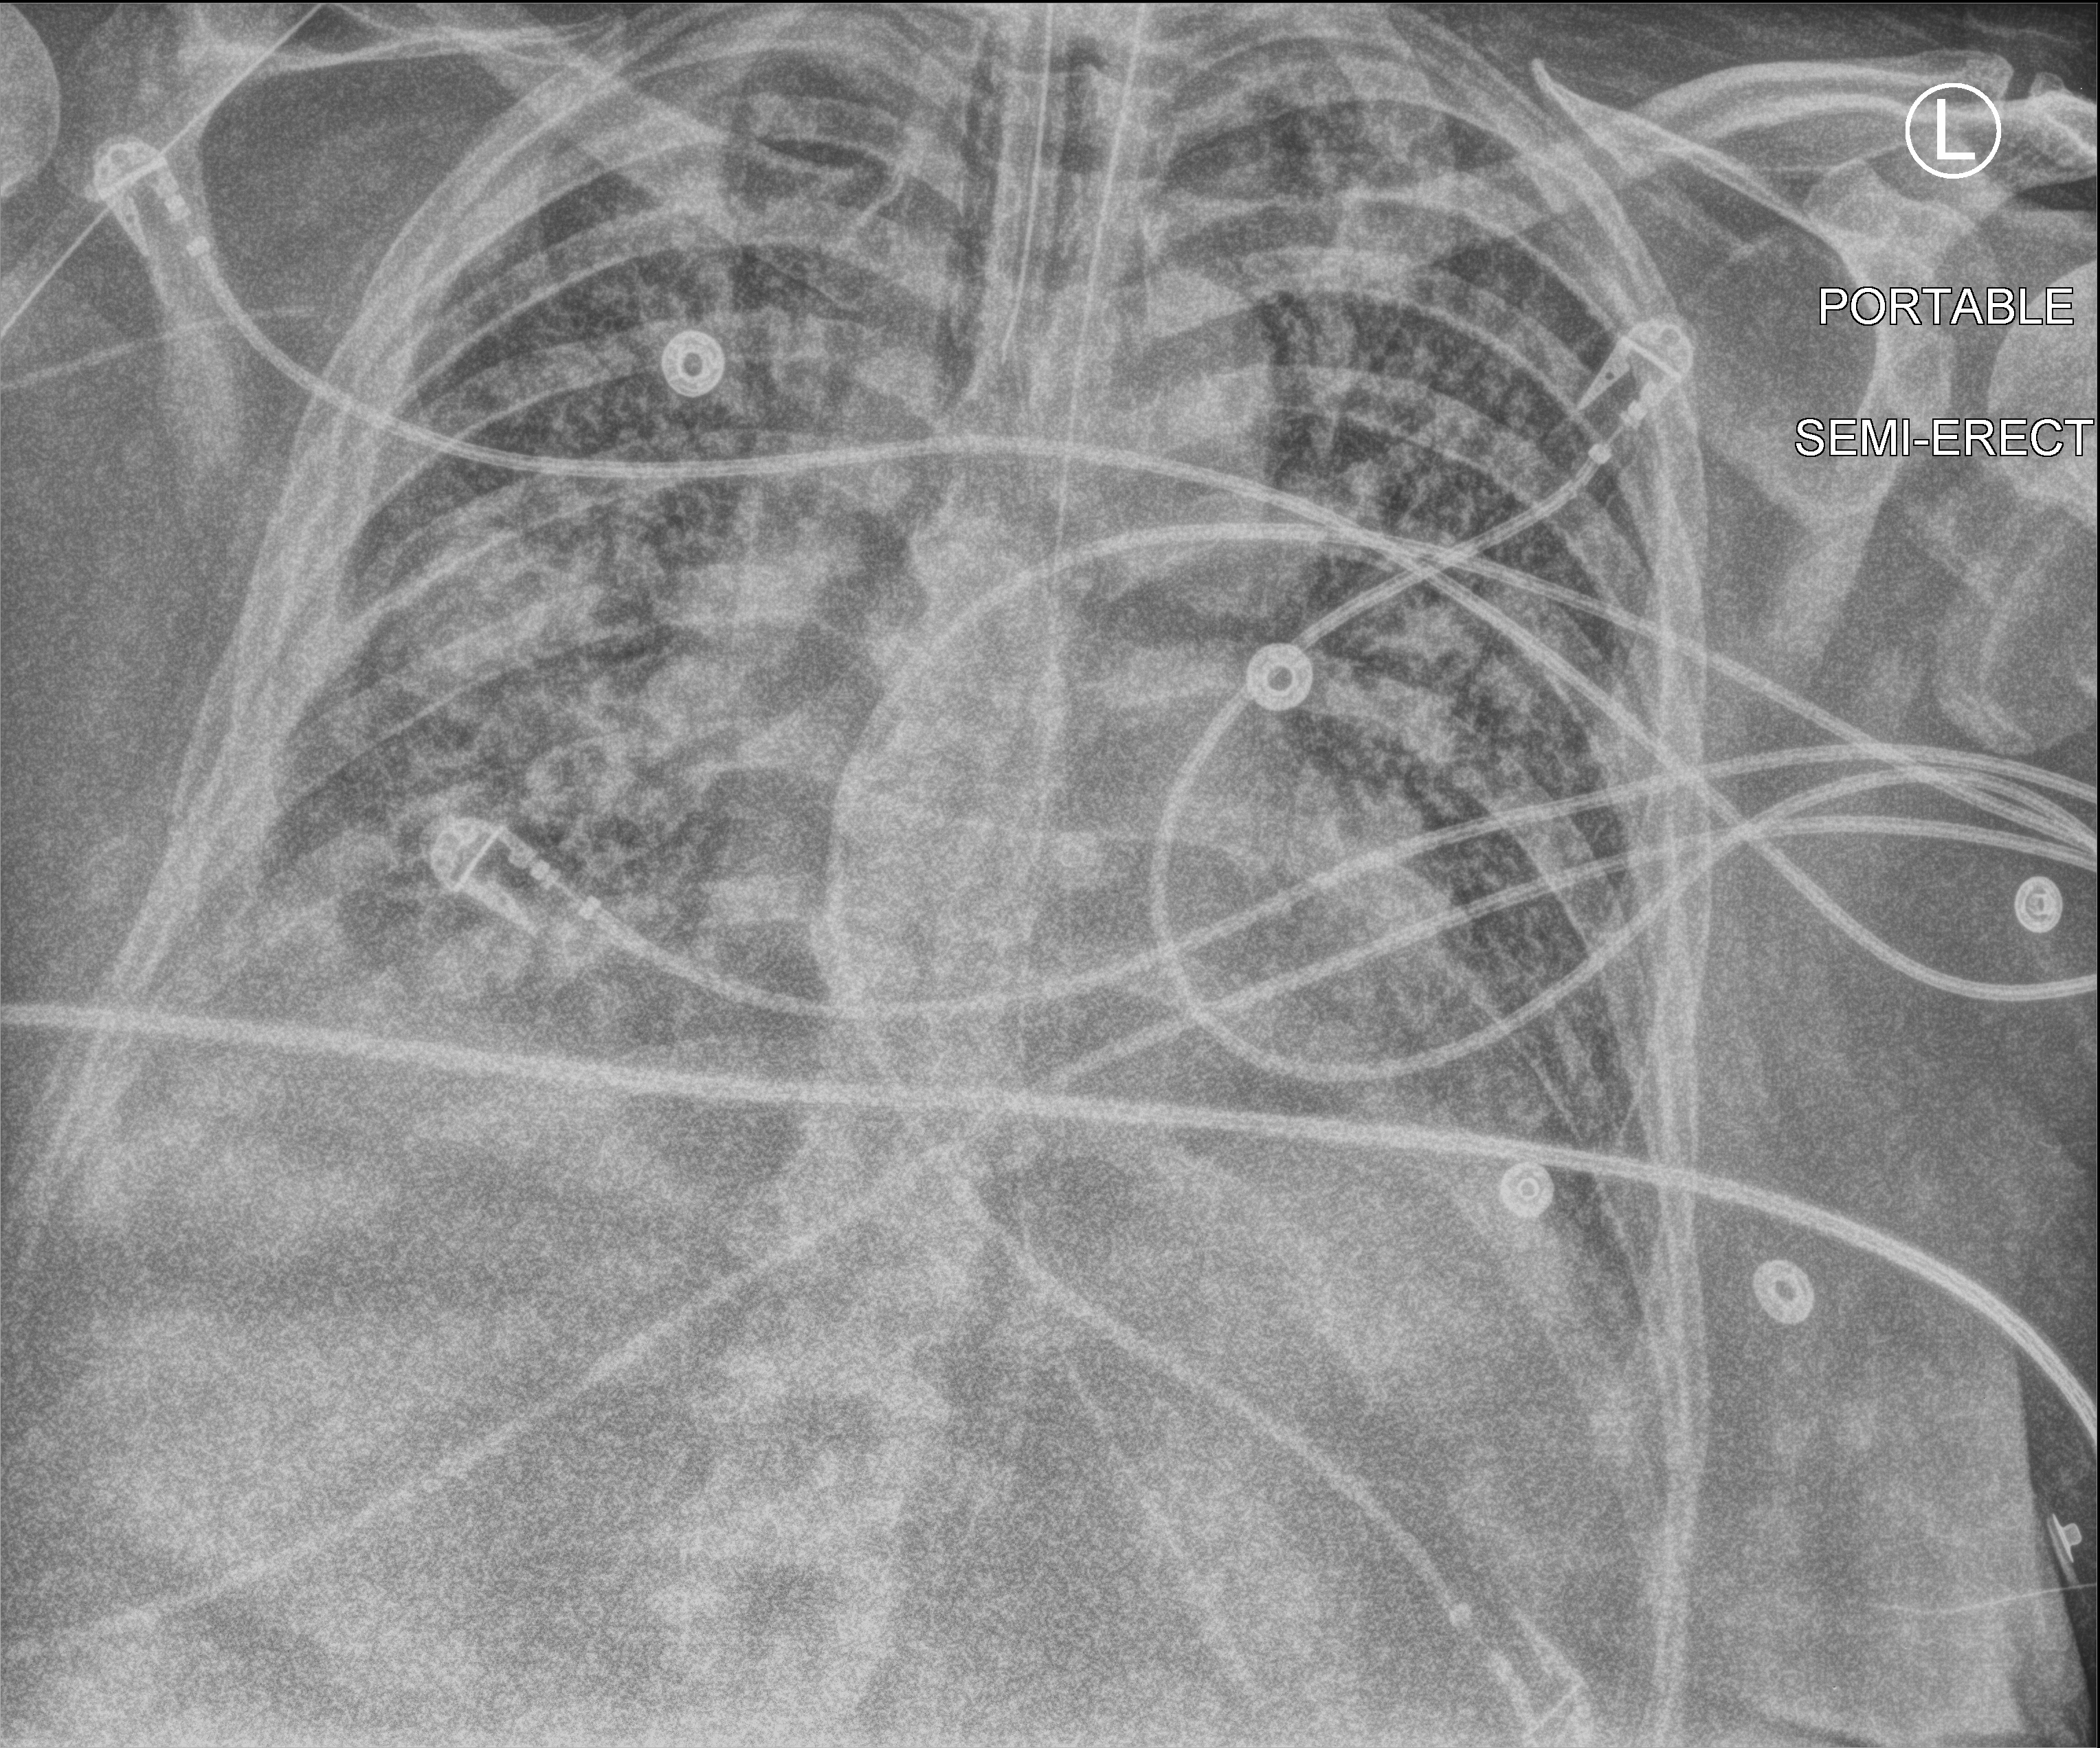
Bedside chest radiograph (computed radiography), anteroposterior (AP) projection. Male patient hospitalised with COVID-19, age 60–74 years.
Admission-level facts for this patient (not findings on this image; timing relative to this image not recorded):
- length of hospital stay: 40 days
- mechanically ventilated during this hospital stay: yes